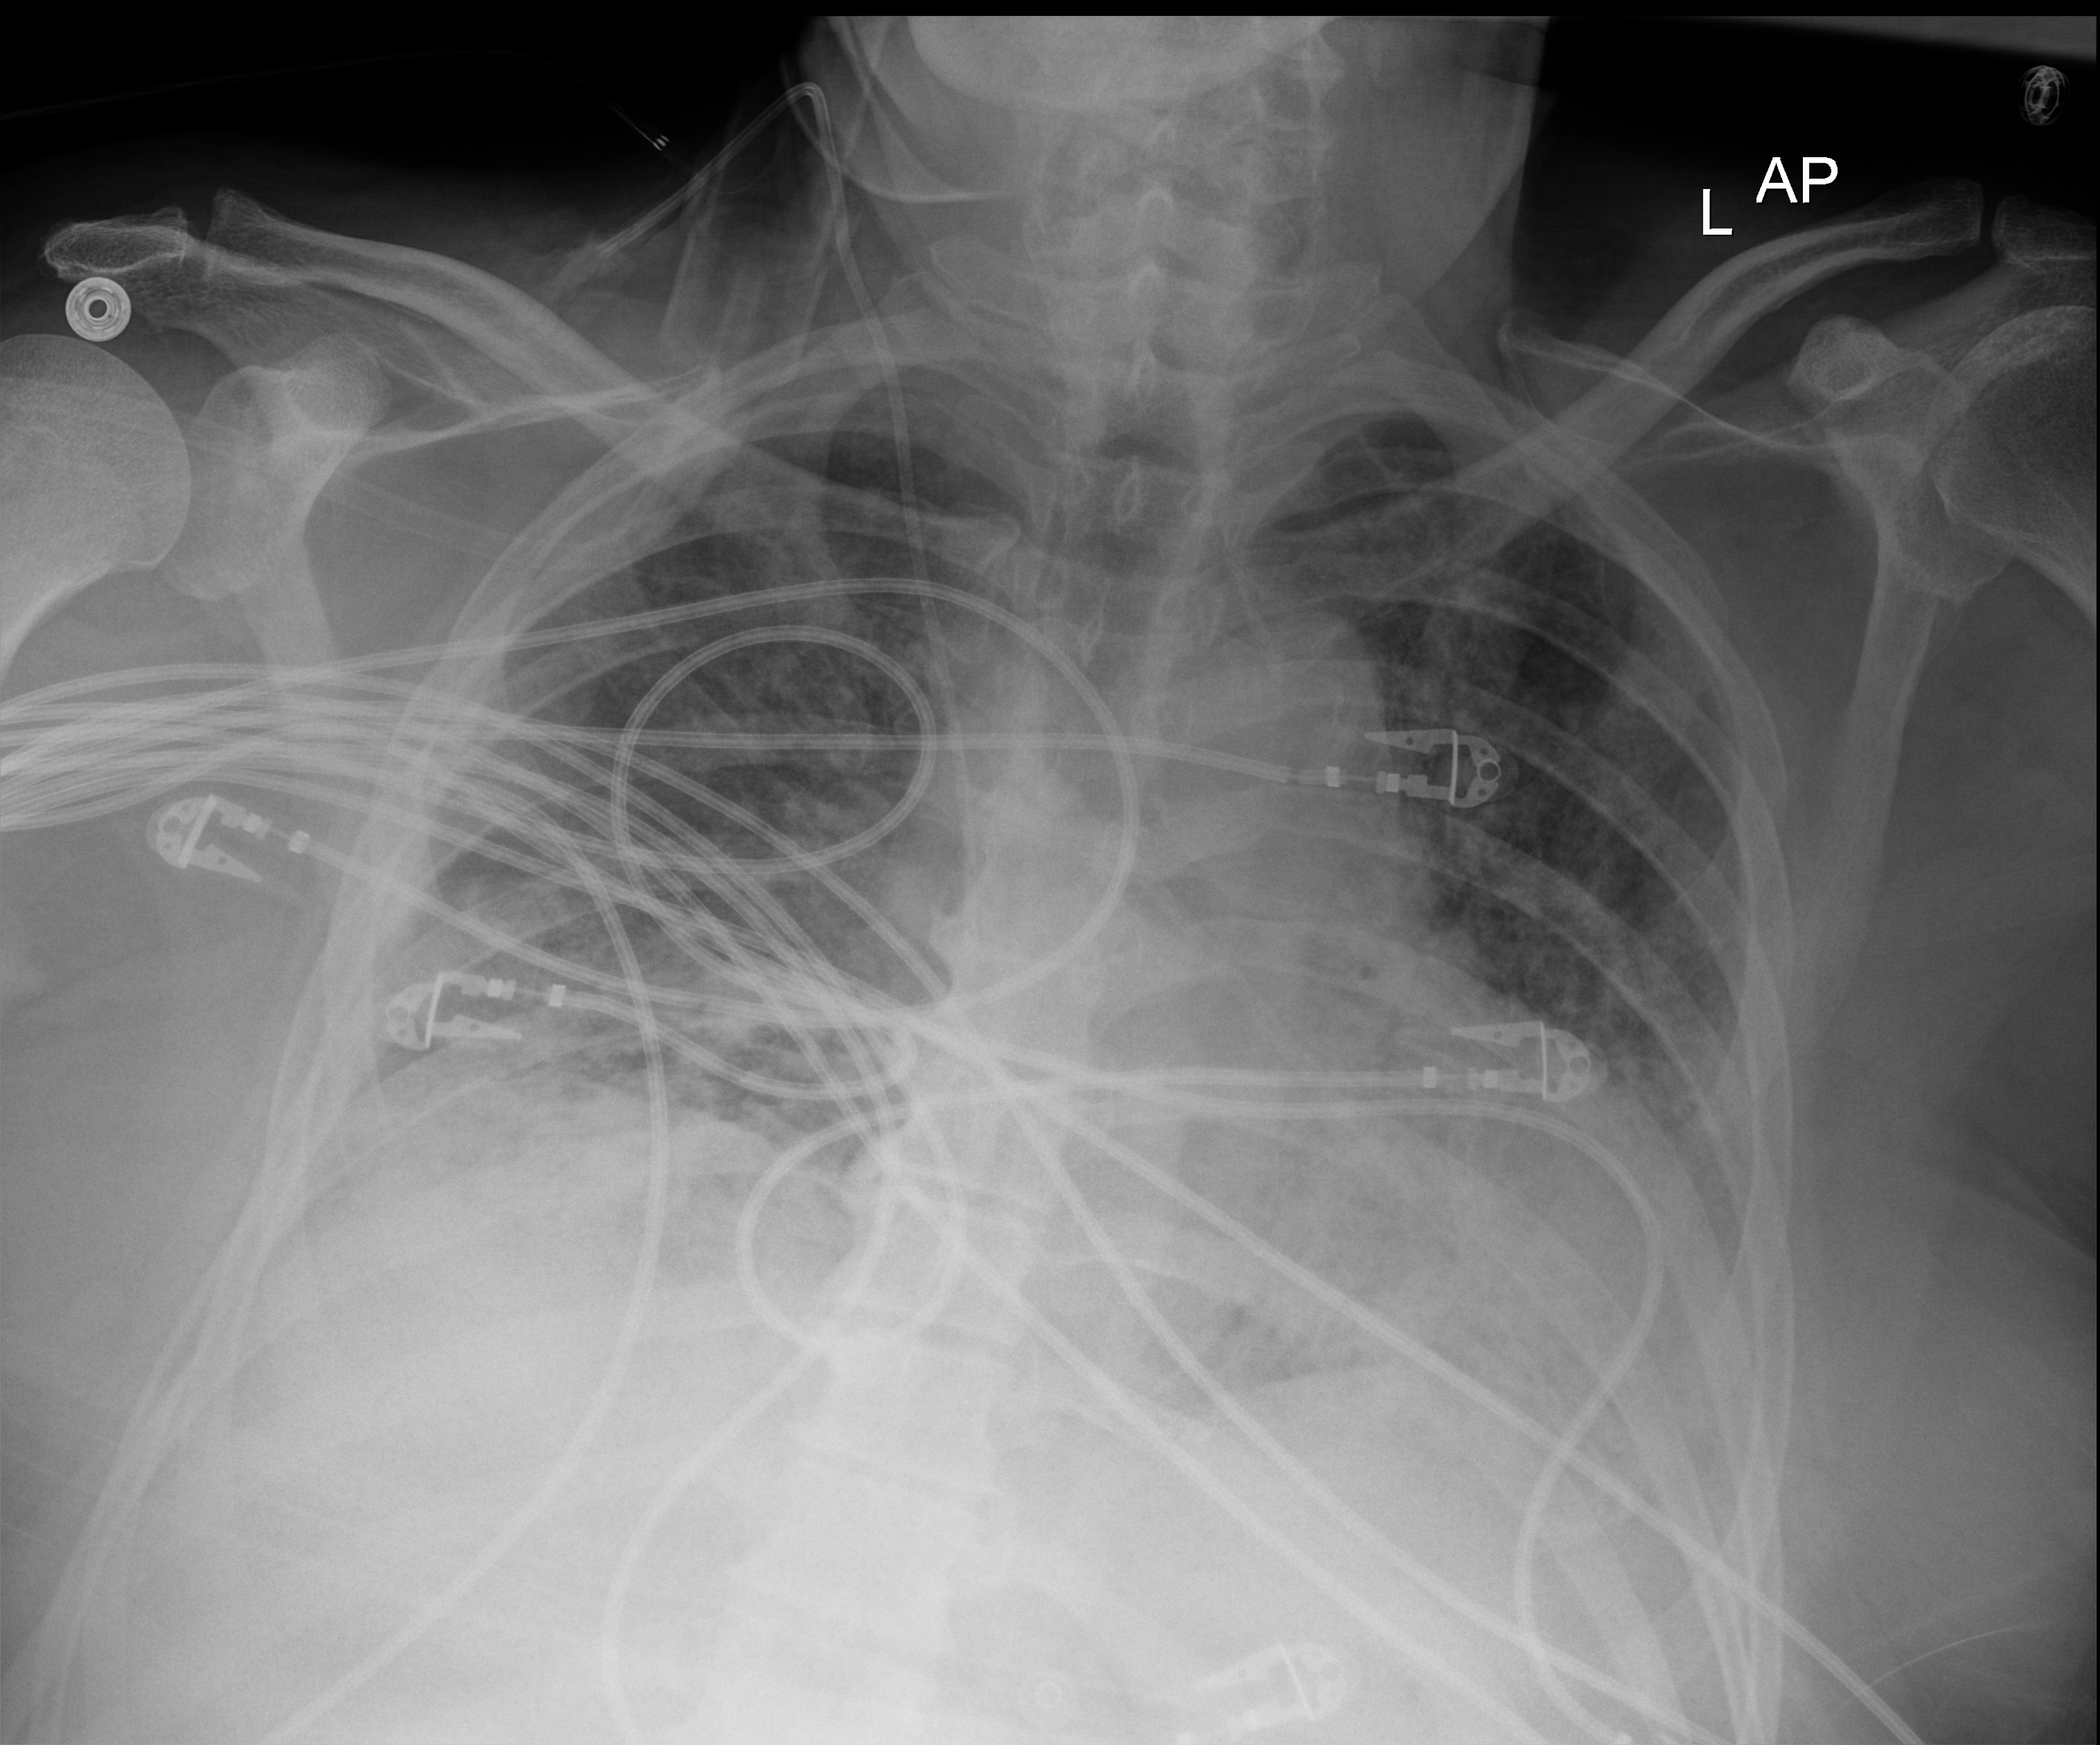
Bedside chest radiograph (digital radiography); anteroposterior (AP) projection. Male patient hospitalised with COVID-19, age 60–74 years.
From the hospital-stay record, not from the radiograph (when in the stay this image was taken is not recorded): smoking status (admission record): former.